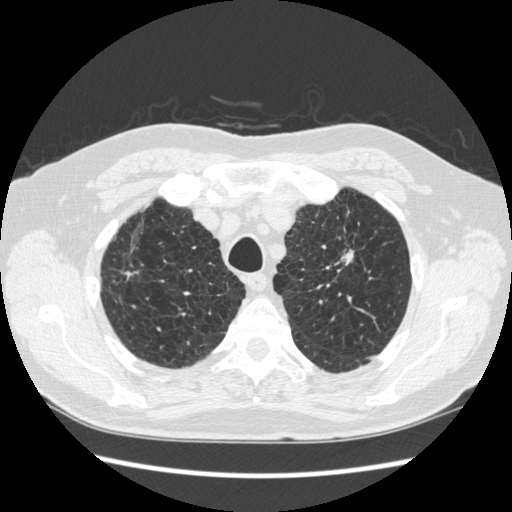
Low-dose screening chest CT, one axial slice. Slice 219 of 267 in the series (ordered by position). 120 kVp. Lung window (W 1500 / L -600 HU). 1.25 mm slice thickness. 512 × 512 image matrix.
Annotated regions visible in this slice (outlined manually by an expert reader):
- lesion 1 (tumor, upper lobe of left lung): box from (x=341, y=250) to (x=354, y=265) px